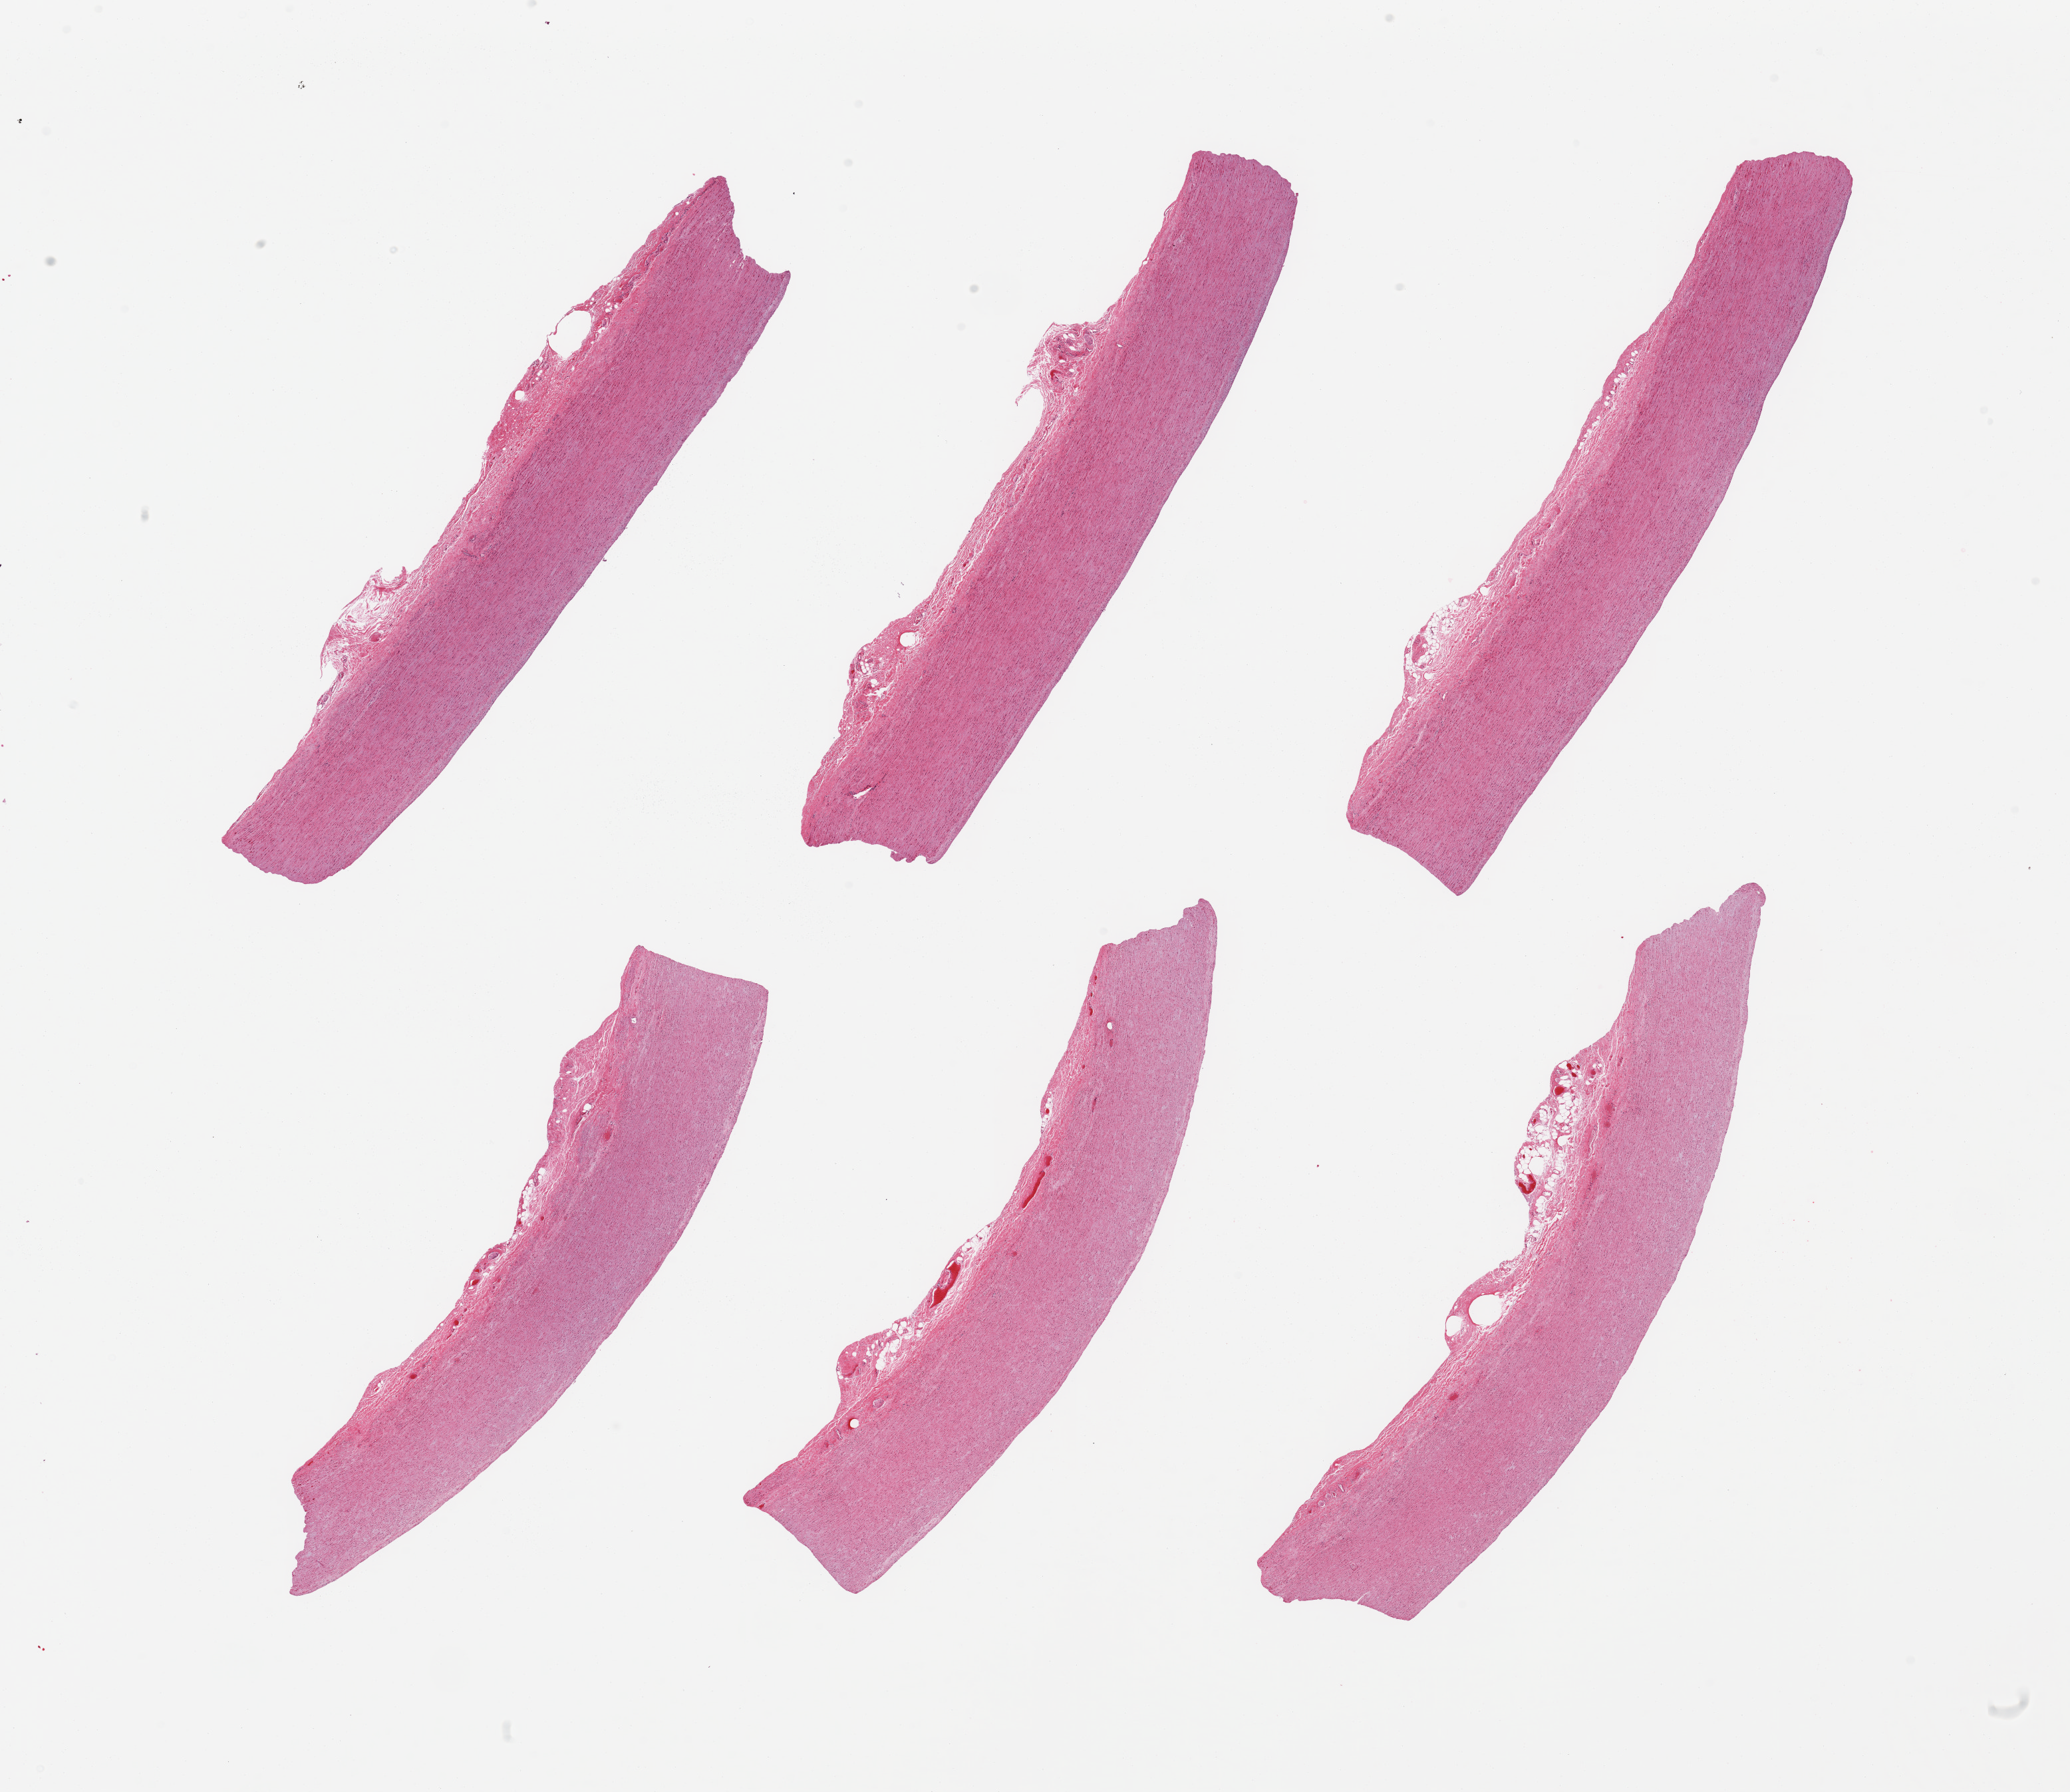
Hematoxylin and eosin (H&E) whole-slide image, brightfield, shown as a low-resolution overview of the whole scanned area (about 24.6 x 21.3 mm, slide scanned at 20x); PAXgene-fixed paraffin-embedded (PFPE) section; sampled site (target tissue): aorta; donor tissue sample.
Pathologist's review note for this sample: 6 pieces; up to 0.5mm attached congested adventitia.